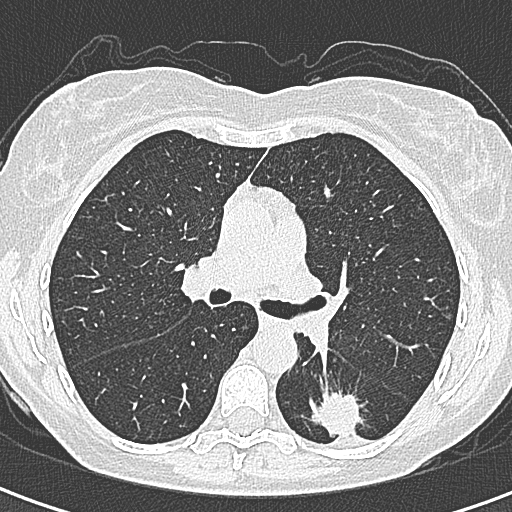
Low-dose screening chest CT, axial slice. Baseline screening round. Lung window (W 1500 / L -600 HU). 1 mm slice thickness. Lung (sharp) reconstruction kernel (B80f). Female participant, aged 58 years at enrolment. Former smoker at enrolment.
- Expert reader's lesion annotation, bounding box (x1, y1, x2, y2) in pixels: (293, 389, 363, 455).
- The screening reader recorded 2 non-calcified nodules or masses ≥4 mm on this exam; which of them this box marks is not recorded.
- Lung cancer was diagnosed 22 days after this screen: adenocarcinoma, NOS, left lower lobe, moderately differentiated (G2), stage IA (AJCC 6th edition), 25 mm at pathology.